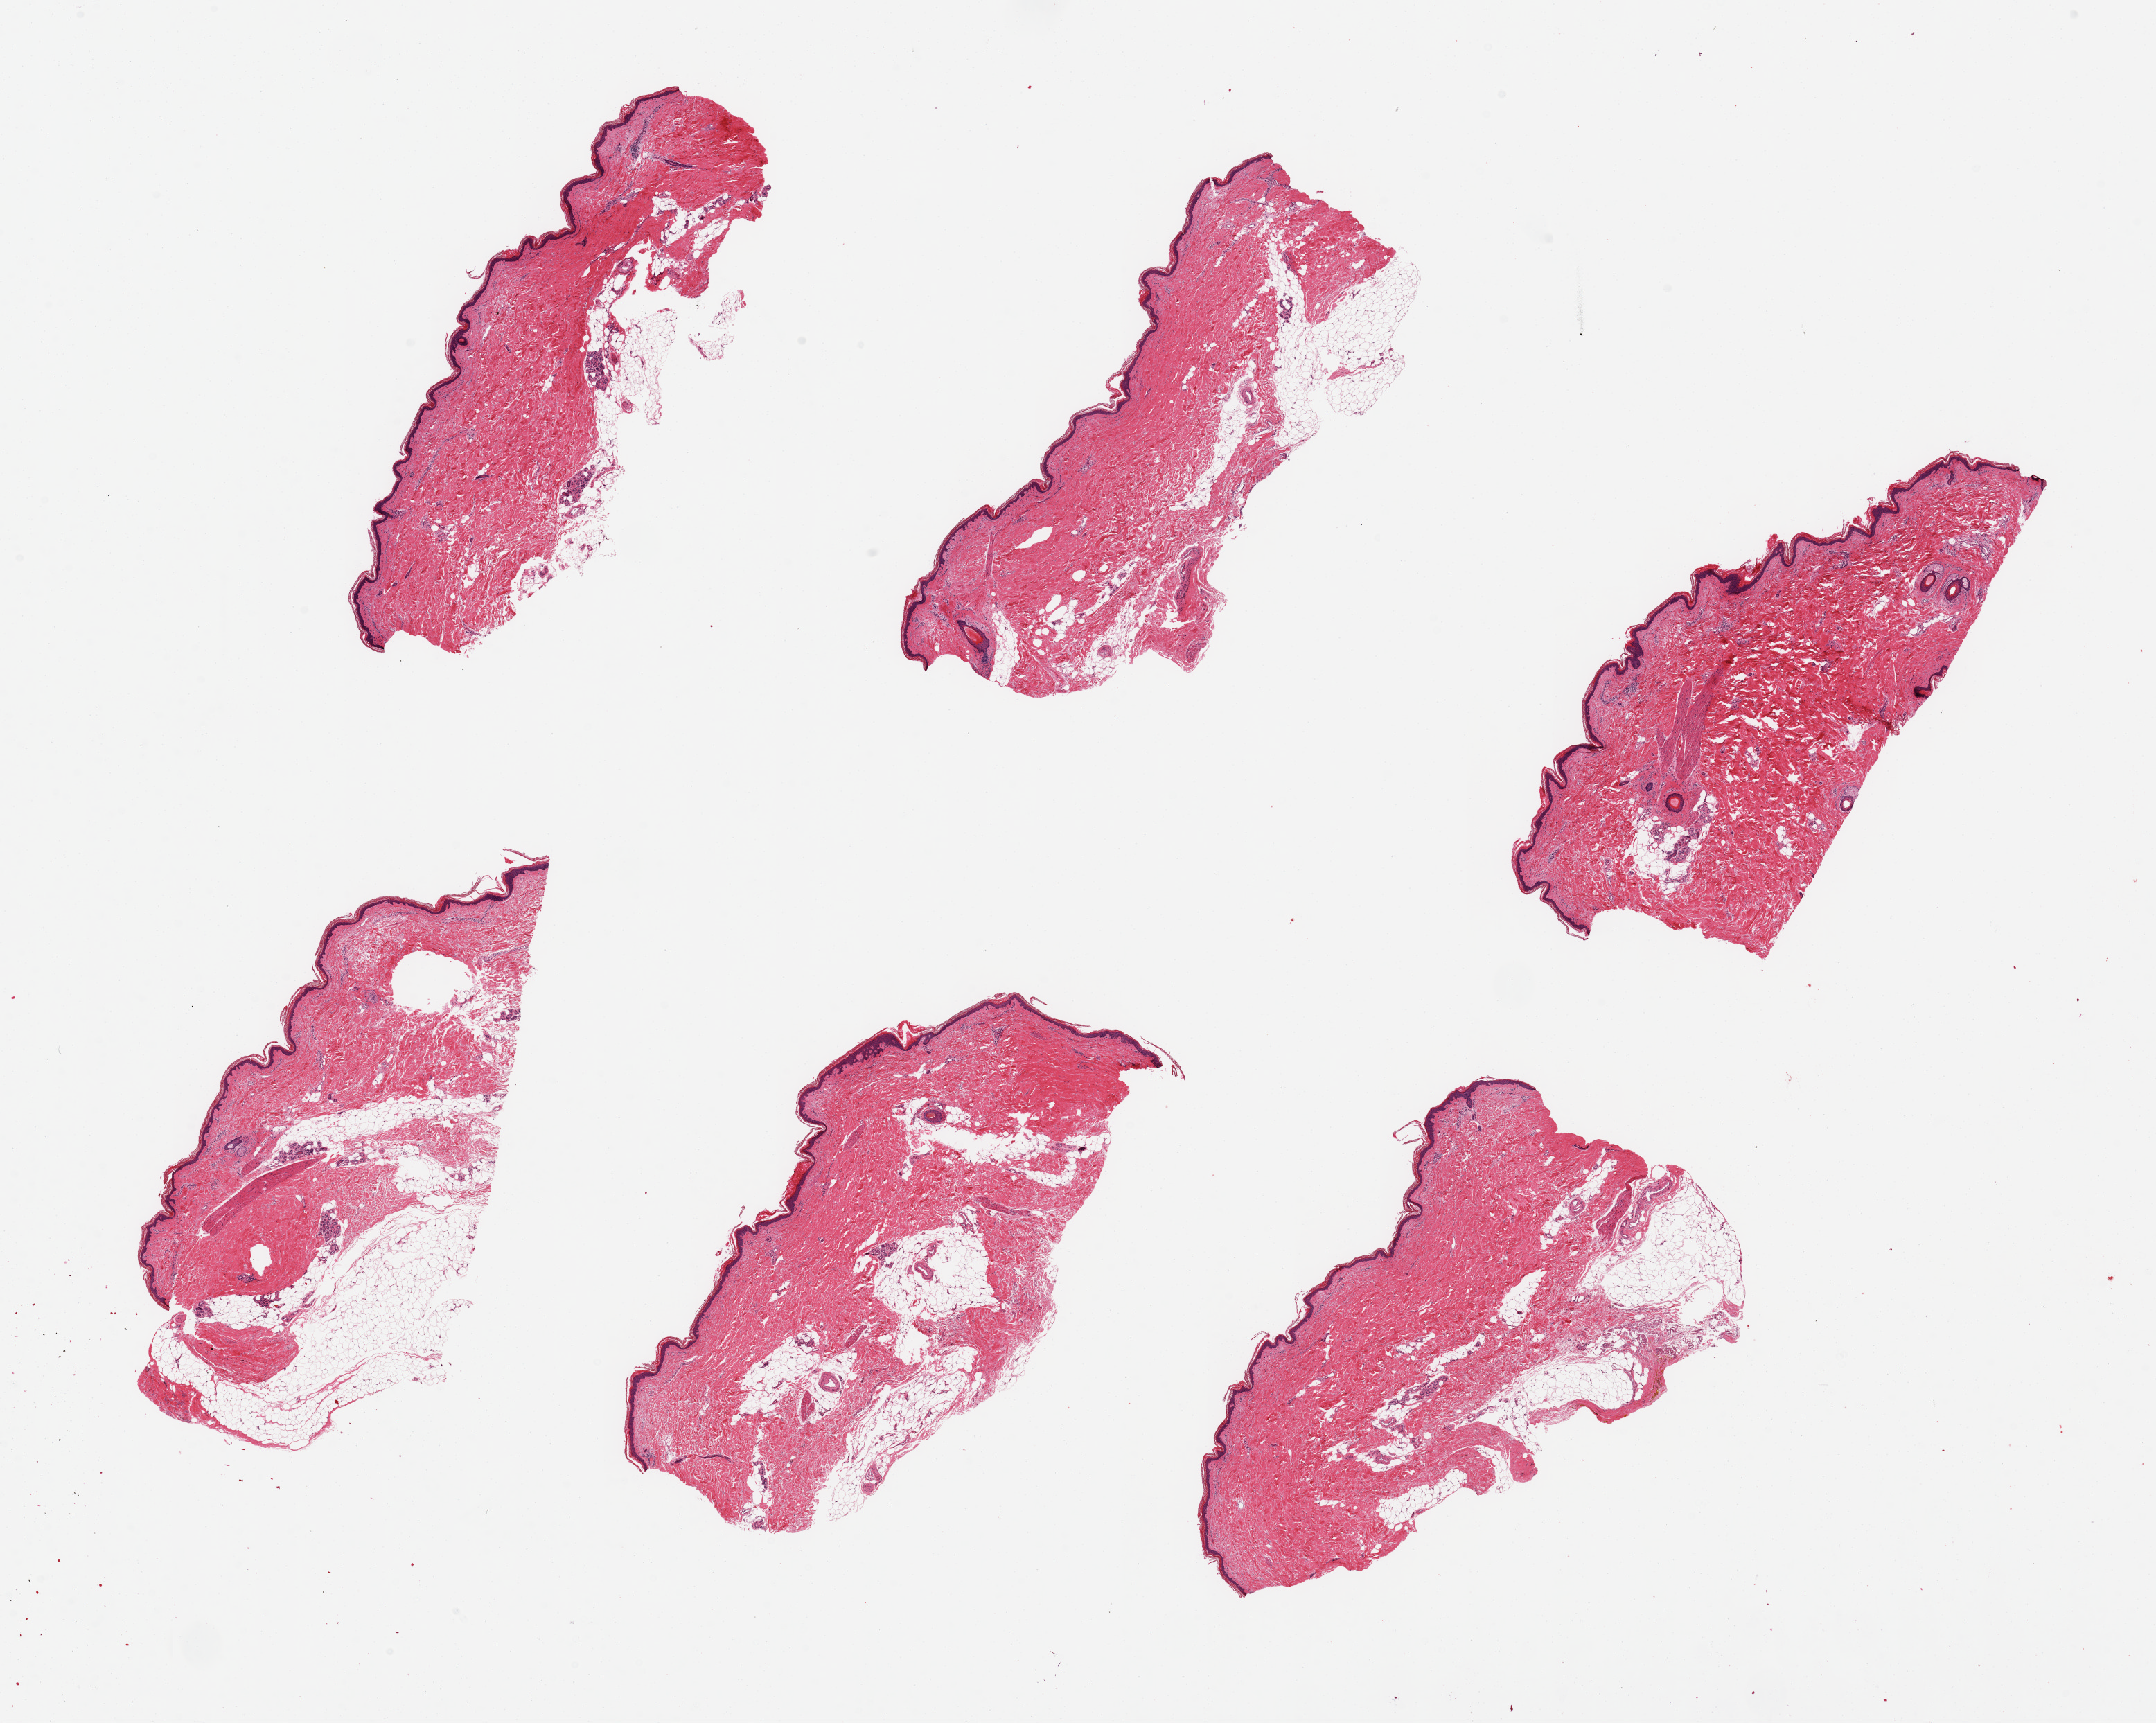
H&E whole-slide image, shown as a low-resolution overview of the whole scanned area (about 24.6 x 19.7 mm, acquisition: 20x scan). PAXgene-fixed paraffin-embedded (PFPE) section. Target tissue: skin of lower leg. Donor tissue sample.
Pathologist's review note for this sample: 6 pieces, ~7x3mm. Squamous epithelium is ~2-3% thickness.